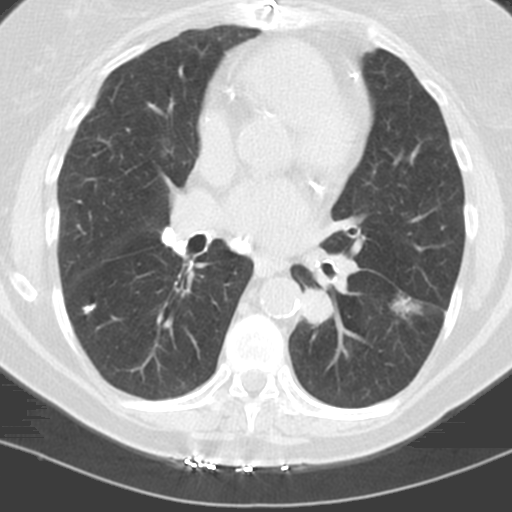
Low-dose screening chest CT, axial slice; first (baseline) screen; lung window (W 1500 / L -600 HU); slice 66 of 121 in the series. Female, age 60 years at enrolment.
2 lesions marked by an expert reader on this slice (largest first), bounding box <372,285,429,333> (left, top, right, bottom; pixels); <291,281,339,332>. The screening reader recorded 3 non-calcified nodules or masses ≥4 mm on this exam (left lower lobe, left lower lobe, right middle lobe); which of them these boxes mark is not recorded. Participant outcome: lung cancer diagnosed 96 days after this screen — adenocarcinoma, NOS, left lower lobe, stage IV (AJCC 6th edition), 22 mm at pathology.